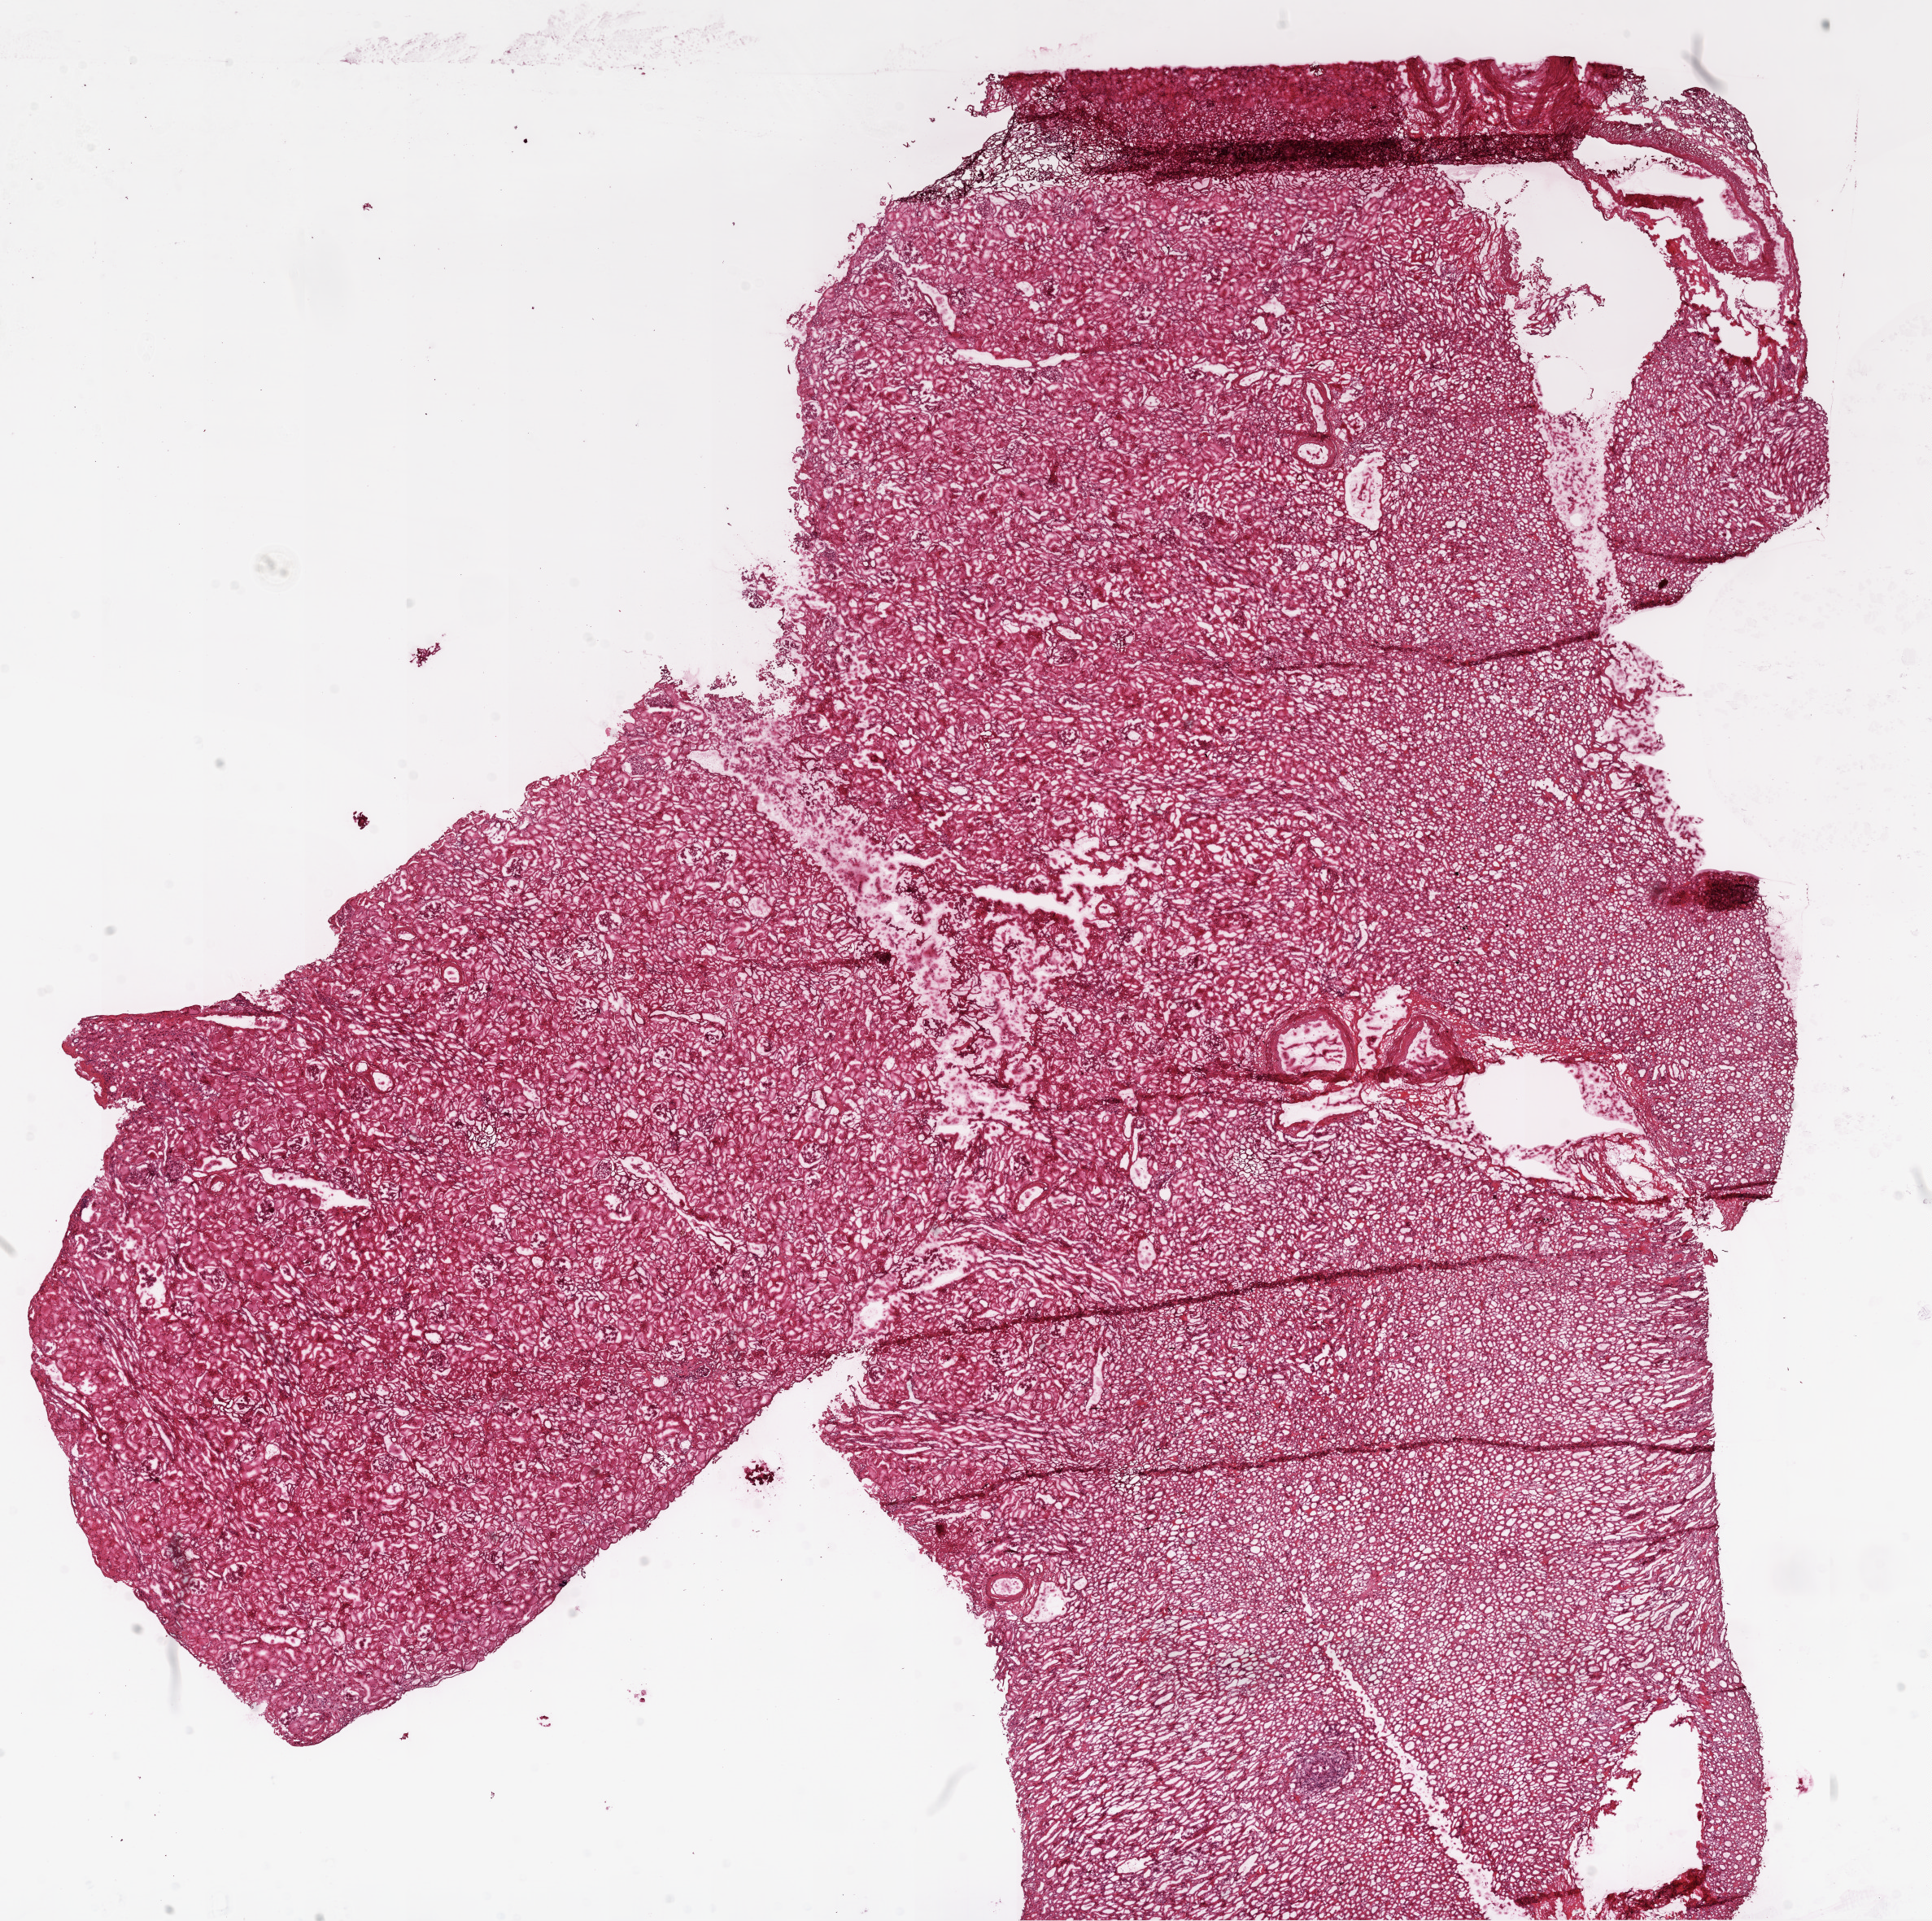
Hematoxylin and eosin (H&E) stained whole-slide image, whole scanned area (about 19.1 x 19.0 mm) shown as a low-resolution overview; frozen section from the top of the tissue portion; sample: solid tissue normal (non-tumour tissue), kidney. Female, age 74 years at initial diagnosis.
This section: solid tissue normal sample (biorepository sample class). Patient diagnosis: Clear cell adenocarcinoma, NOS.